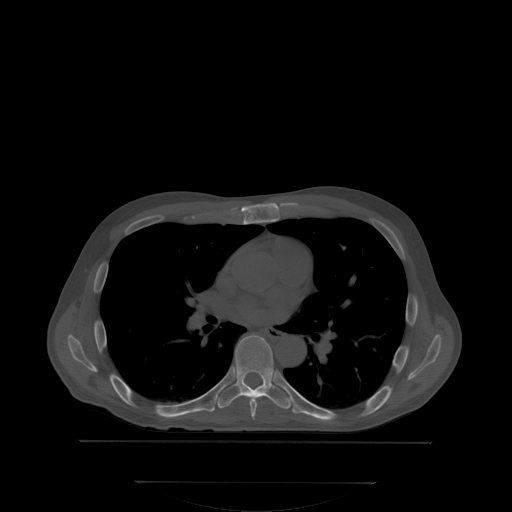
CT including the spine, one axial slice. Position 229 of 350 along the scan axis. Bone window (W 1800 / L 400 HU). 512 × 512 image matrix, field of view 500 × 500 mm. Male patient, age 58 years. From the clinical record (not read from this slice): primary cancer: prostate; vertebrae with lytic lesions (as recorded): L1.
Structures marked on this image (semi-automatic segmentation, software-assisted and operator-edited):
- T6 vertebra: bounding box [x1, y1, x2, y2] px = [250, 400, 257, 417]
- T7 vertebra: [205, 335, 292, 411]